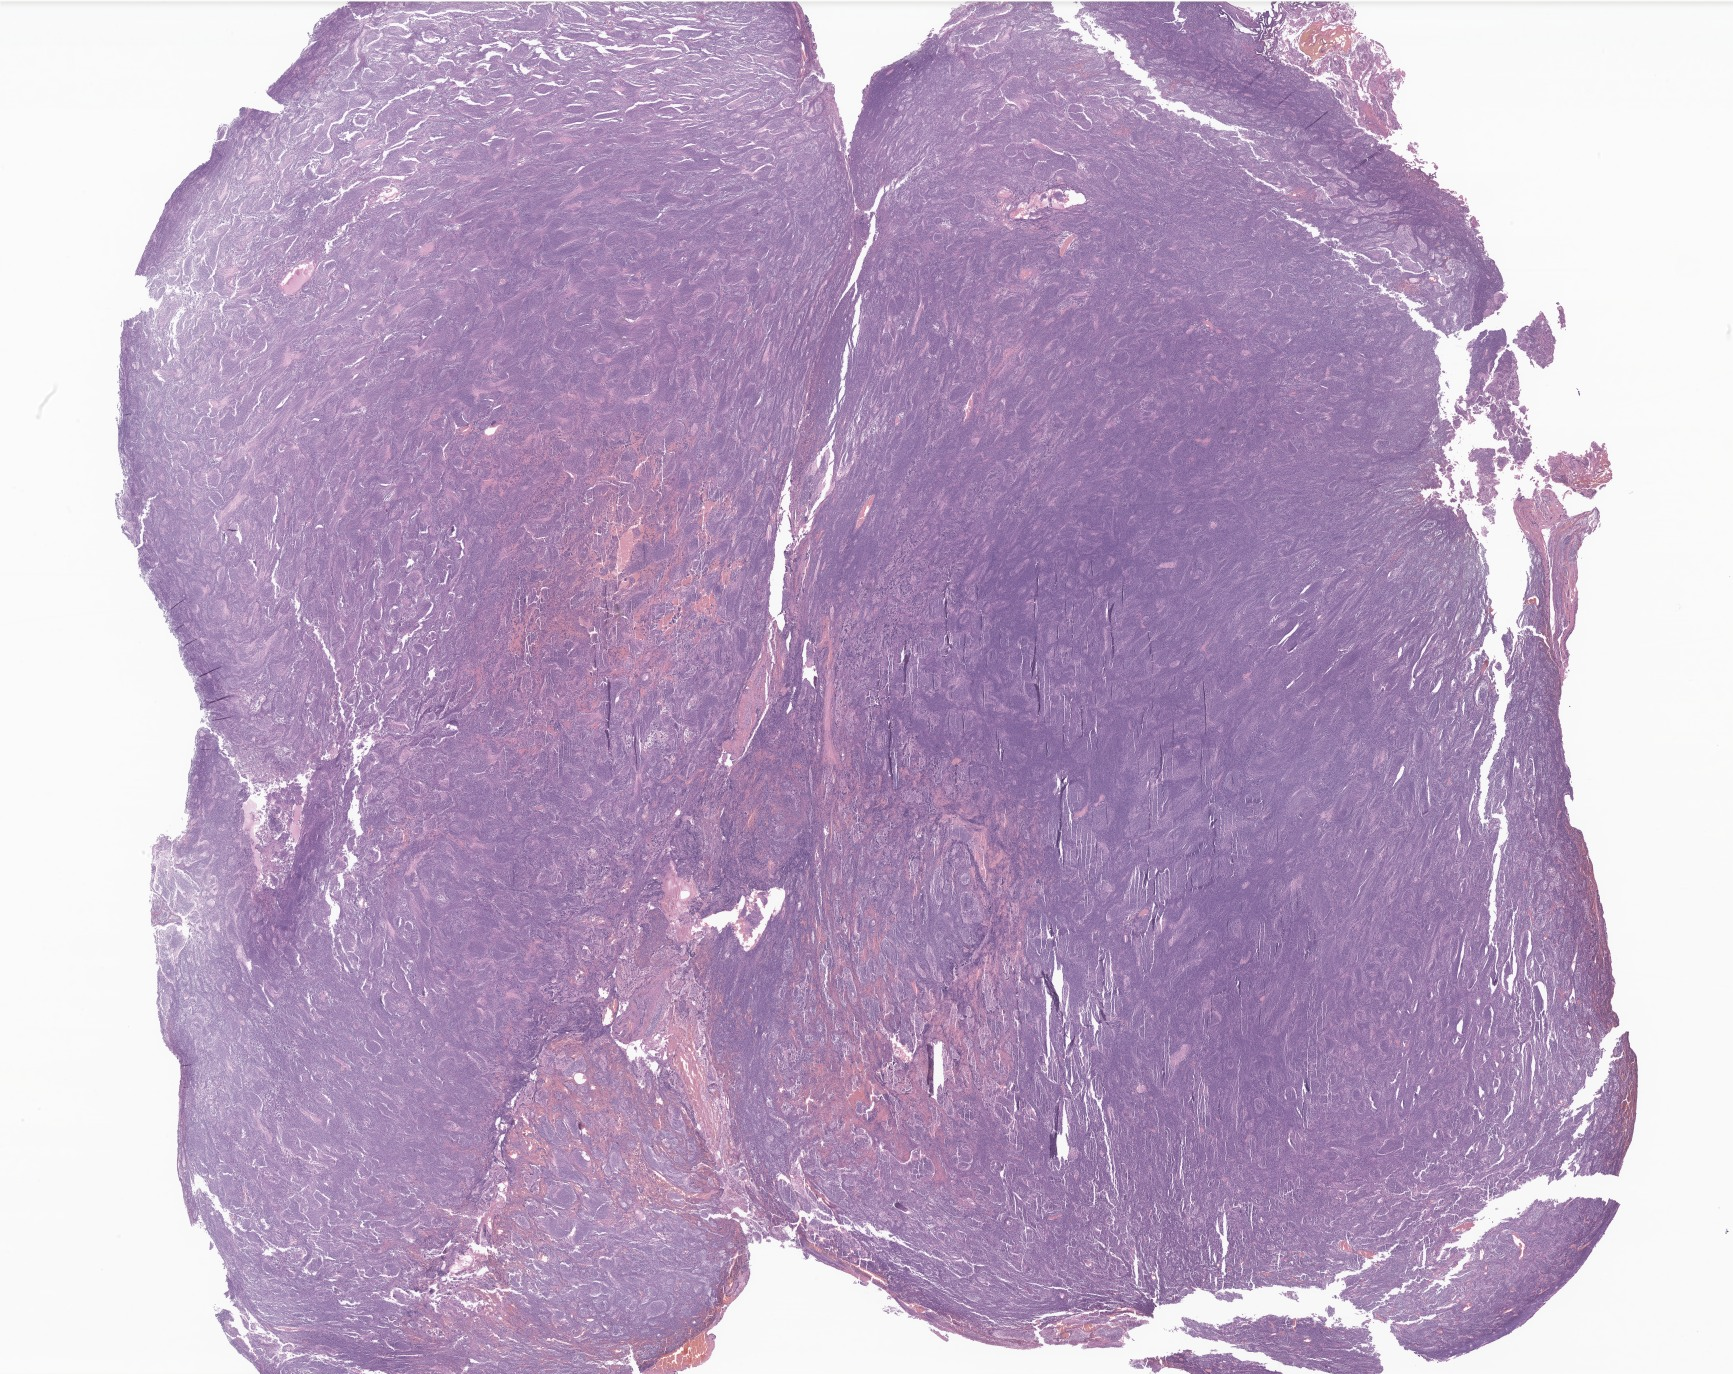
H&E whole-slide image of tumor tissue from the cerebellum — shown as a low-resolution overview of the whole scanned area (about 29.2 x 23.2 mm), FFPE section. Patient: female, age 391 days (about 1.1 years).
* diagnosis (ICD-O-3 morphology term): Desmoplastic nodular medulloblastoma